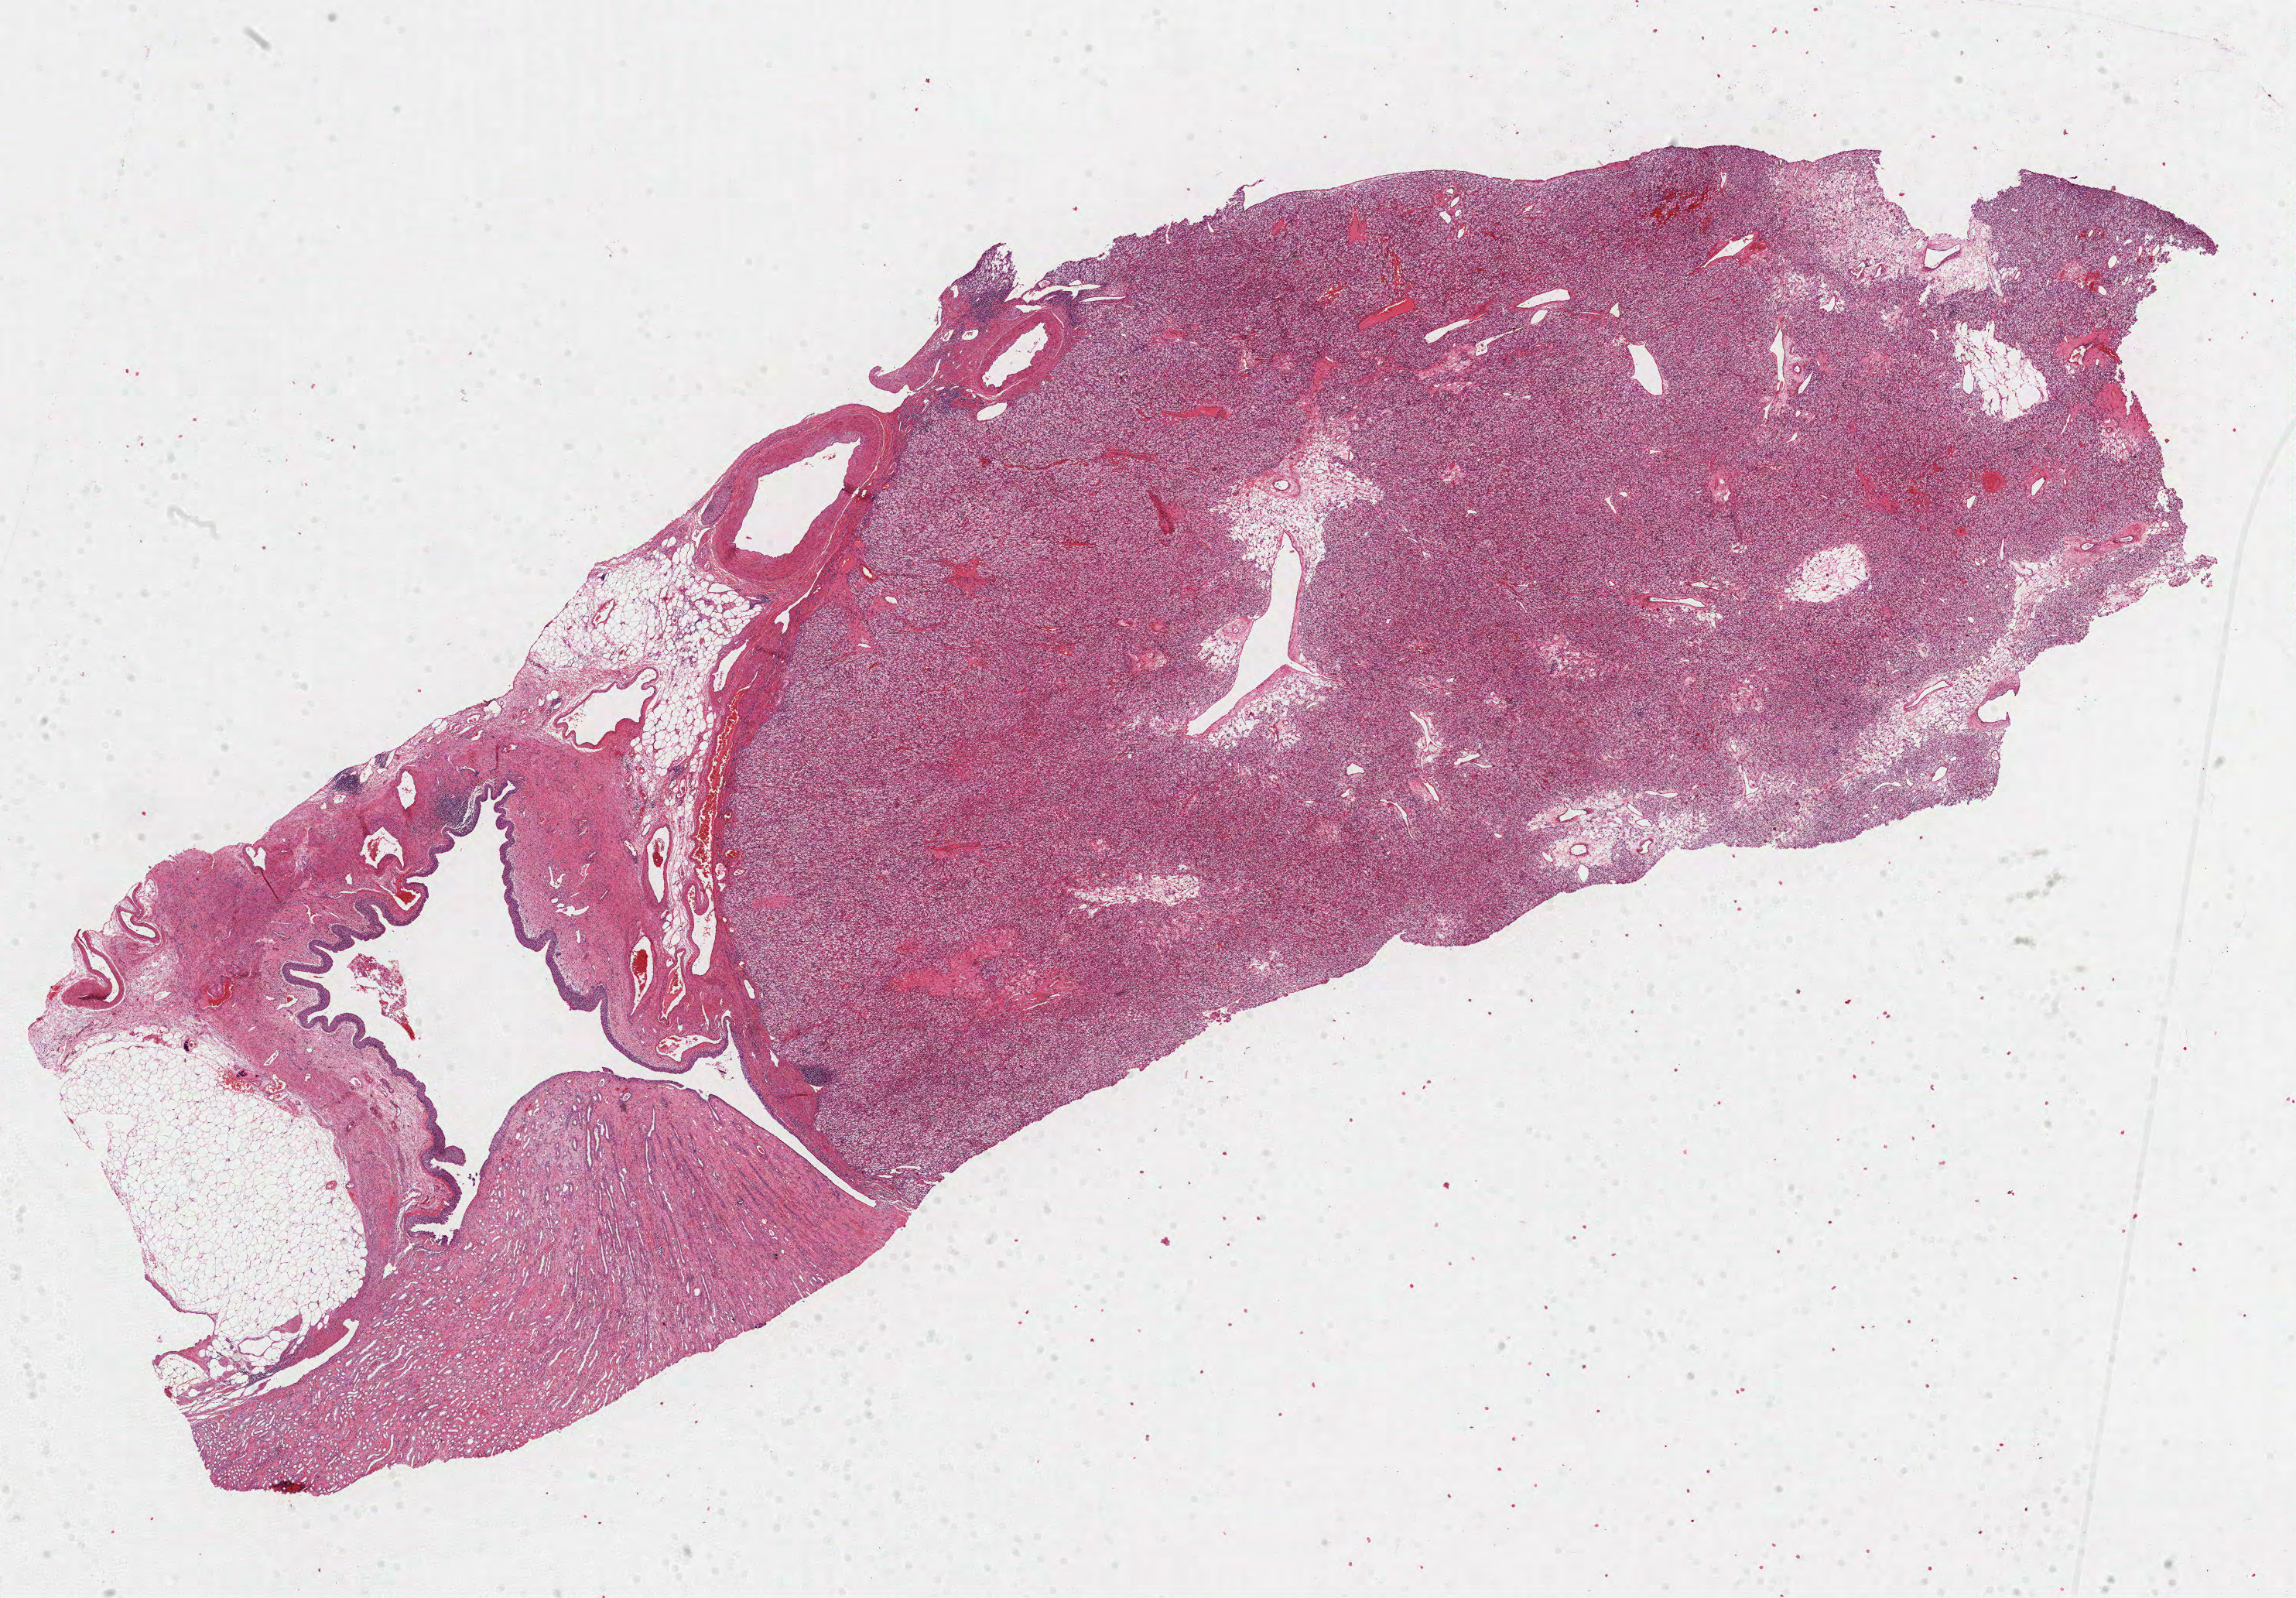
Digitized Hematoxylin and eosin (H&E) stained tissue section (whole slide), a low-resolution overview of the entire scanned area, about 23.9 x 16.7 mm; formalin-fixed paraffin-embedded (FFPE) diagnostic section; kidney, primary tumour sample. Female patient; age at initial diagnosis 68 years.
Histologic diagnosis: Clear cell adenocarcinoma, NOS.